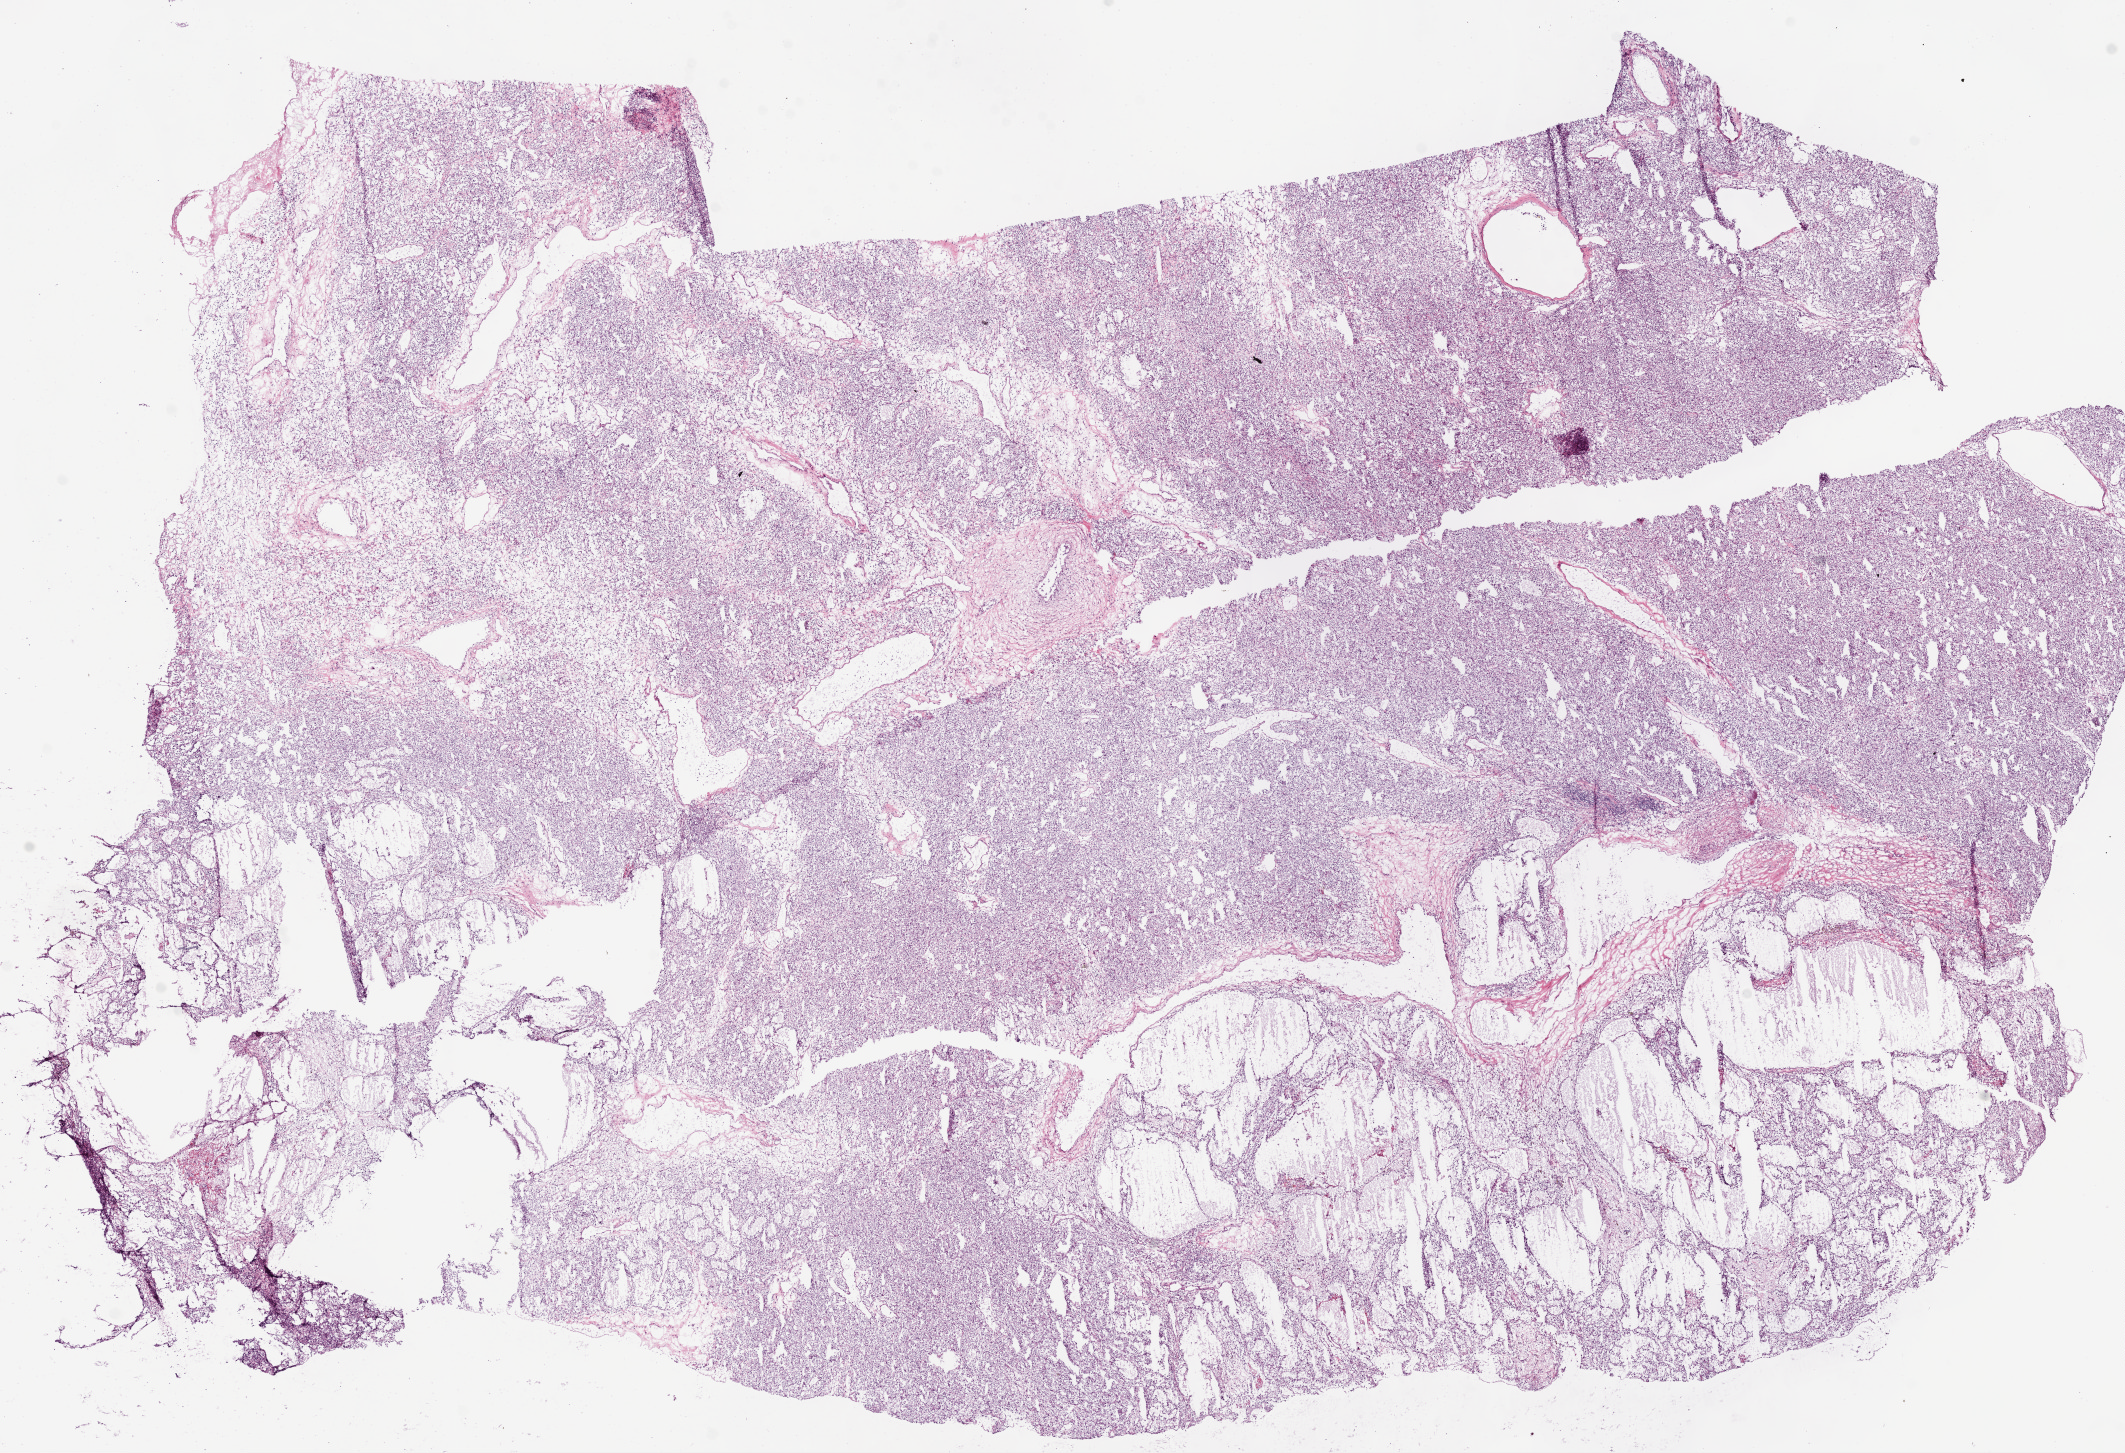
Whole-slide histology image, H&E, low-resolution overview of the scanned area, about 17.1 x 11.7 mm (slide scanned at 20x); frozen section from the bottom of the tissue portion; primary tumour sample from the kidney. Female patient; age at initial diagnosis 86 years. Histologic grade: G4 (undifferentiated). Composition of this section per pathologist review: tumour cells 90%, tumour nuclei 85%, normal cells 0%, stromal cells 10%, necrosis 0%.
Pathologic diagnosis: Clear cell adenocarcinoma, NOS. AJCC pathologic stage: III. TNM: T3a N0 M0. Lymph nodes positive (case pathology): 0 of 2 examined.